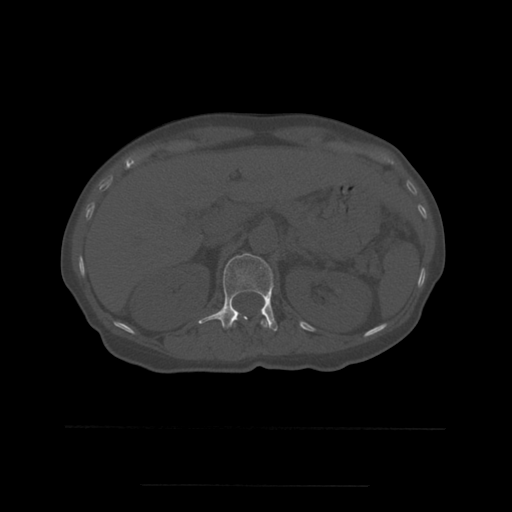
CT including the spine, one axial slice; position 242 of 544 along the scan axis; bone window (W 1800 / L 400 HU); 1.25 mm slice thickness; 512 × 512 image matrix, field of view 350 × 350 mm. Patient age 58 years. Case-level facts recorded for this patient, not image findings: primary cancer: lung.
Annotated regions visible in this slice (semi-automatic segmentation, software-assisted and operator-edited):
- L1 vertebra: bounding box <199,253,278,332> (left, top, right, bottom; pixels)
- T12 vertebra: <234,318,269,328>